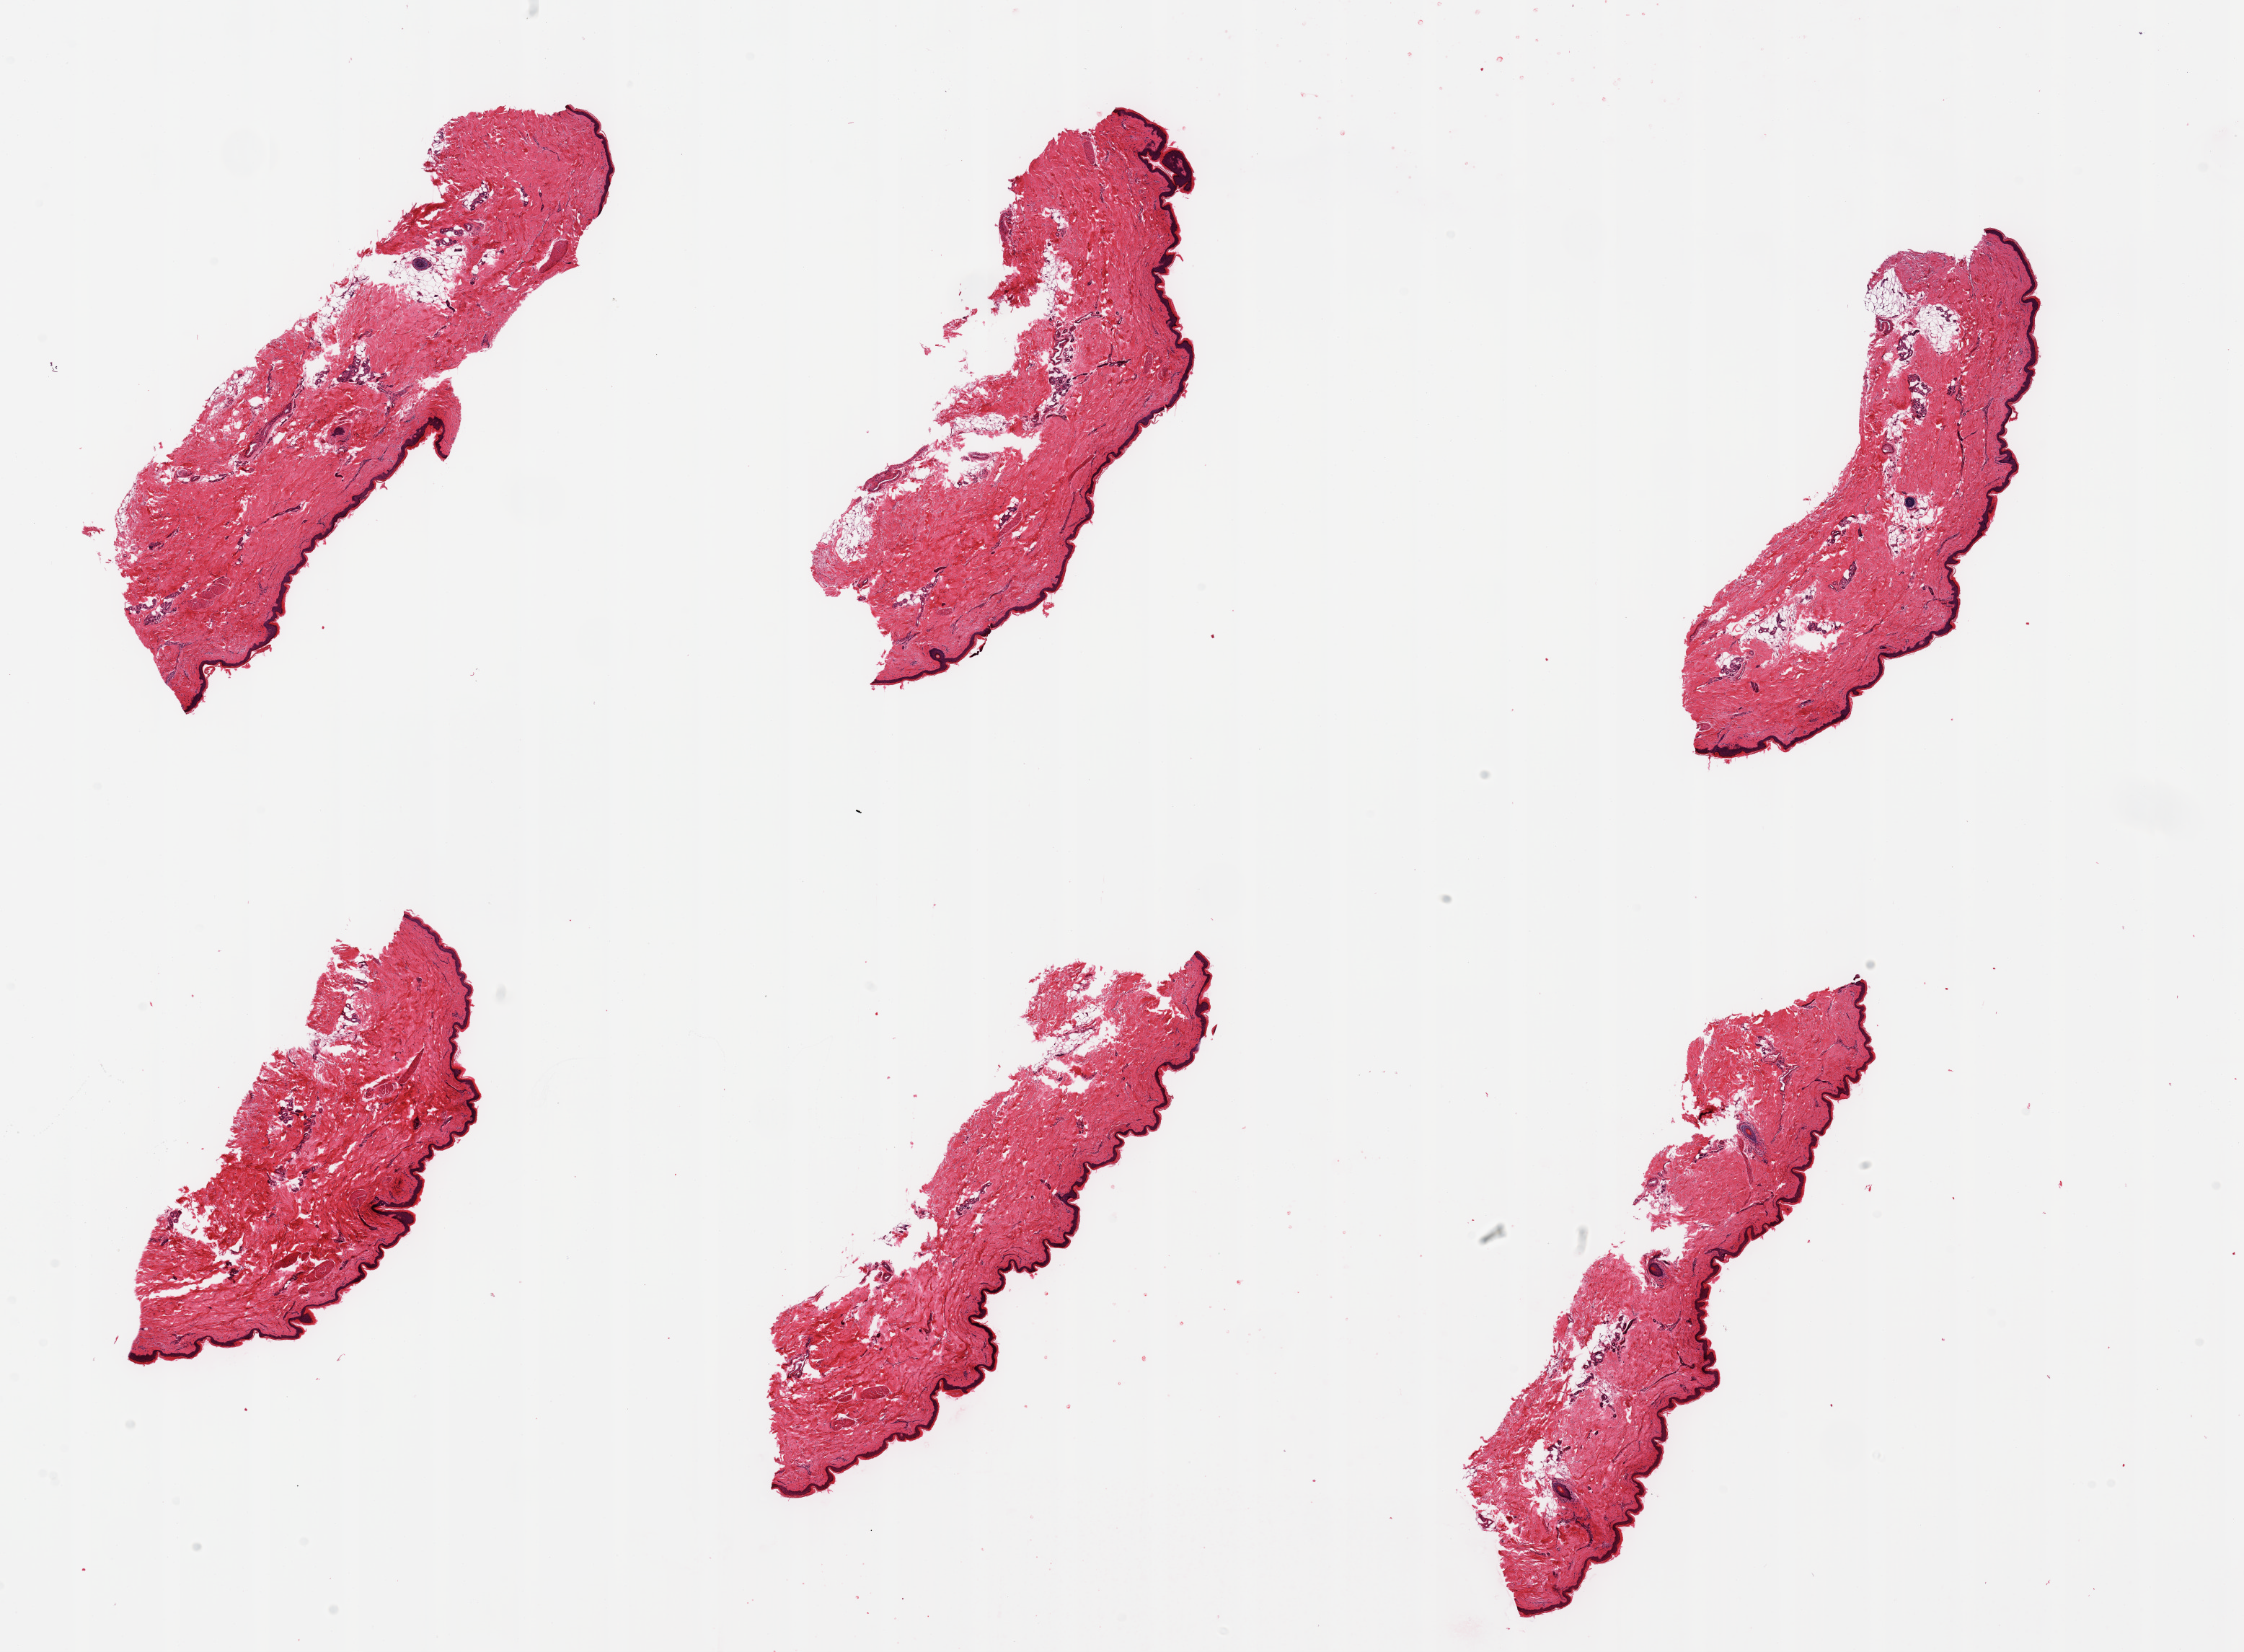
Digitized H&E-stained section — a low-resolution overview of the entire scanned area, about 24.6 x 18.1 mm. PAXgene-fixed, paraffin-embedded tissue. Sampled site (target tissue): skin of lower leg. Tissue donor sample. Donor: female.
Review note (as recorded): 6 pieces; well trimmed; up to 10% dermal fat.